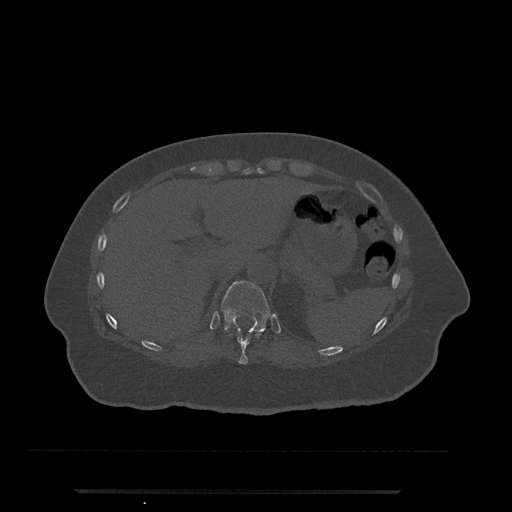
CT including the spine, one axial slice; slice 251 of 797 in the series (ordered by position); reconstruction kernel Br40s/3; 120 kVp; bone window (W 1800 / L 400 HU); 0.5 mm slice thickness; 512 × 512 image matrix, field of view 440 × 440 mm. Patient: female, 51 years. Case-level facts recorded for this patient, not image findings: primary cancer: neuro; vertebrae with lytic lesions (as recorded): T8.
Annotated regions visible in this slice (semi-automatically segmented with operator editing):
- T10 vertebra: box from (x=230, y=330) to (x=265, y=365) px
- T11 vertebra: (x=221, y=281)–(x=270, y=334)